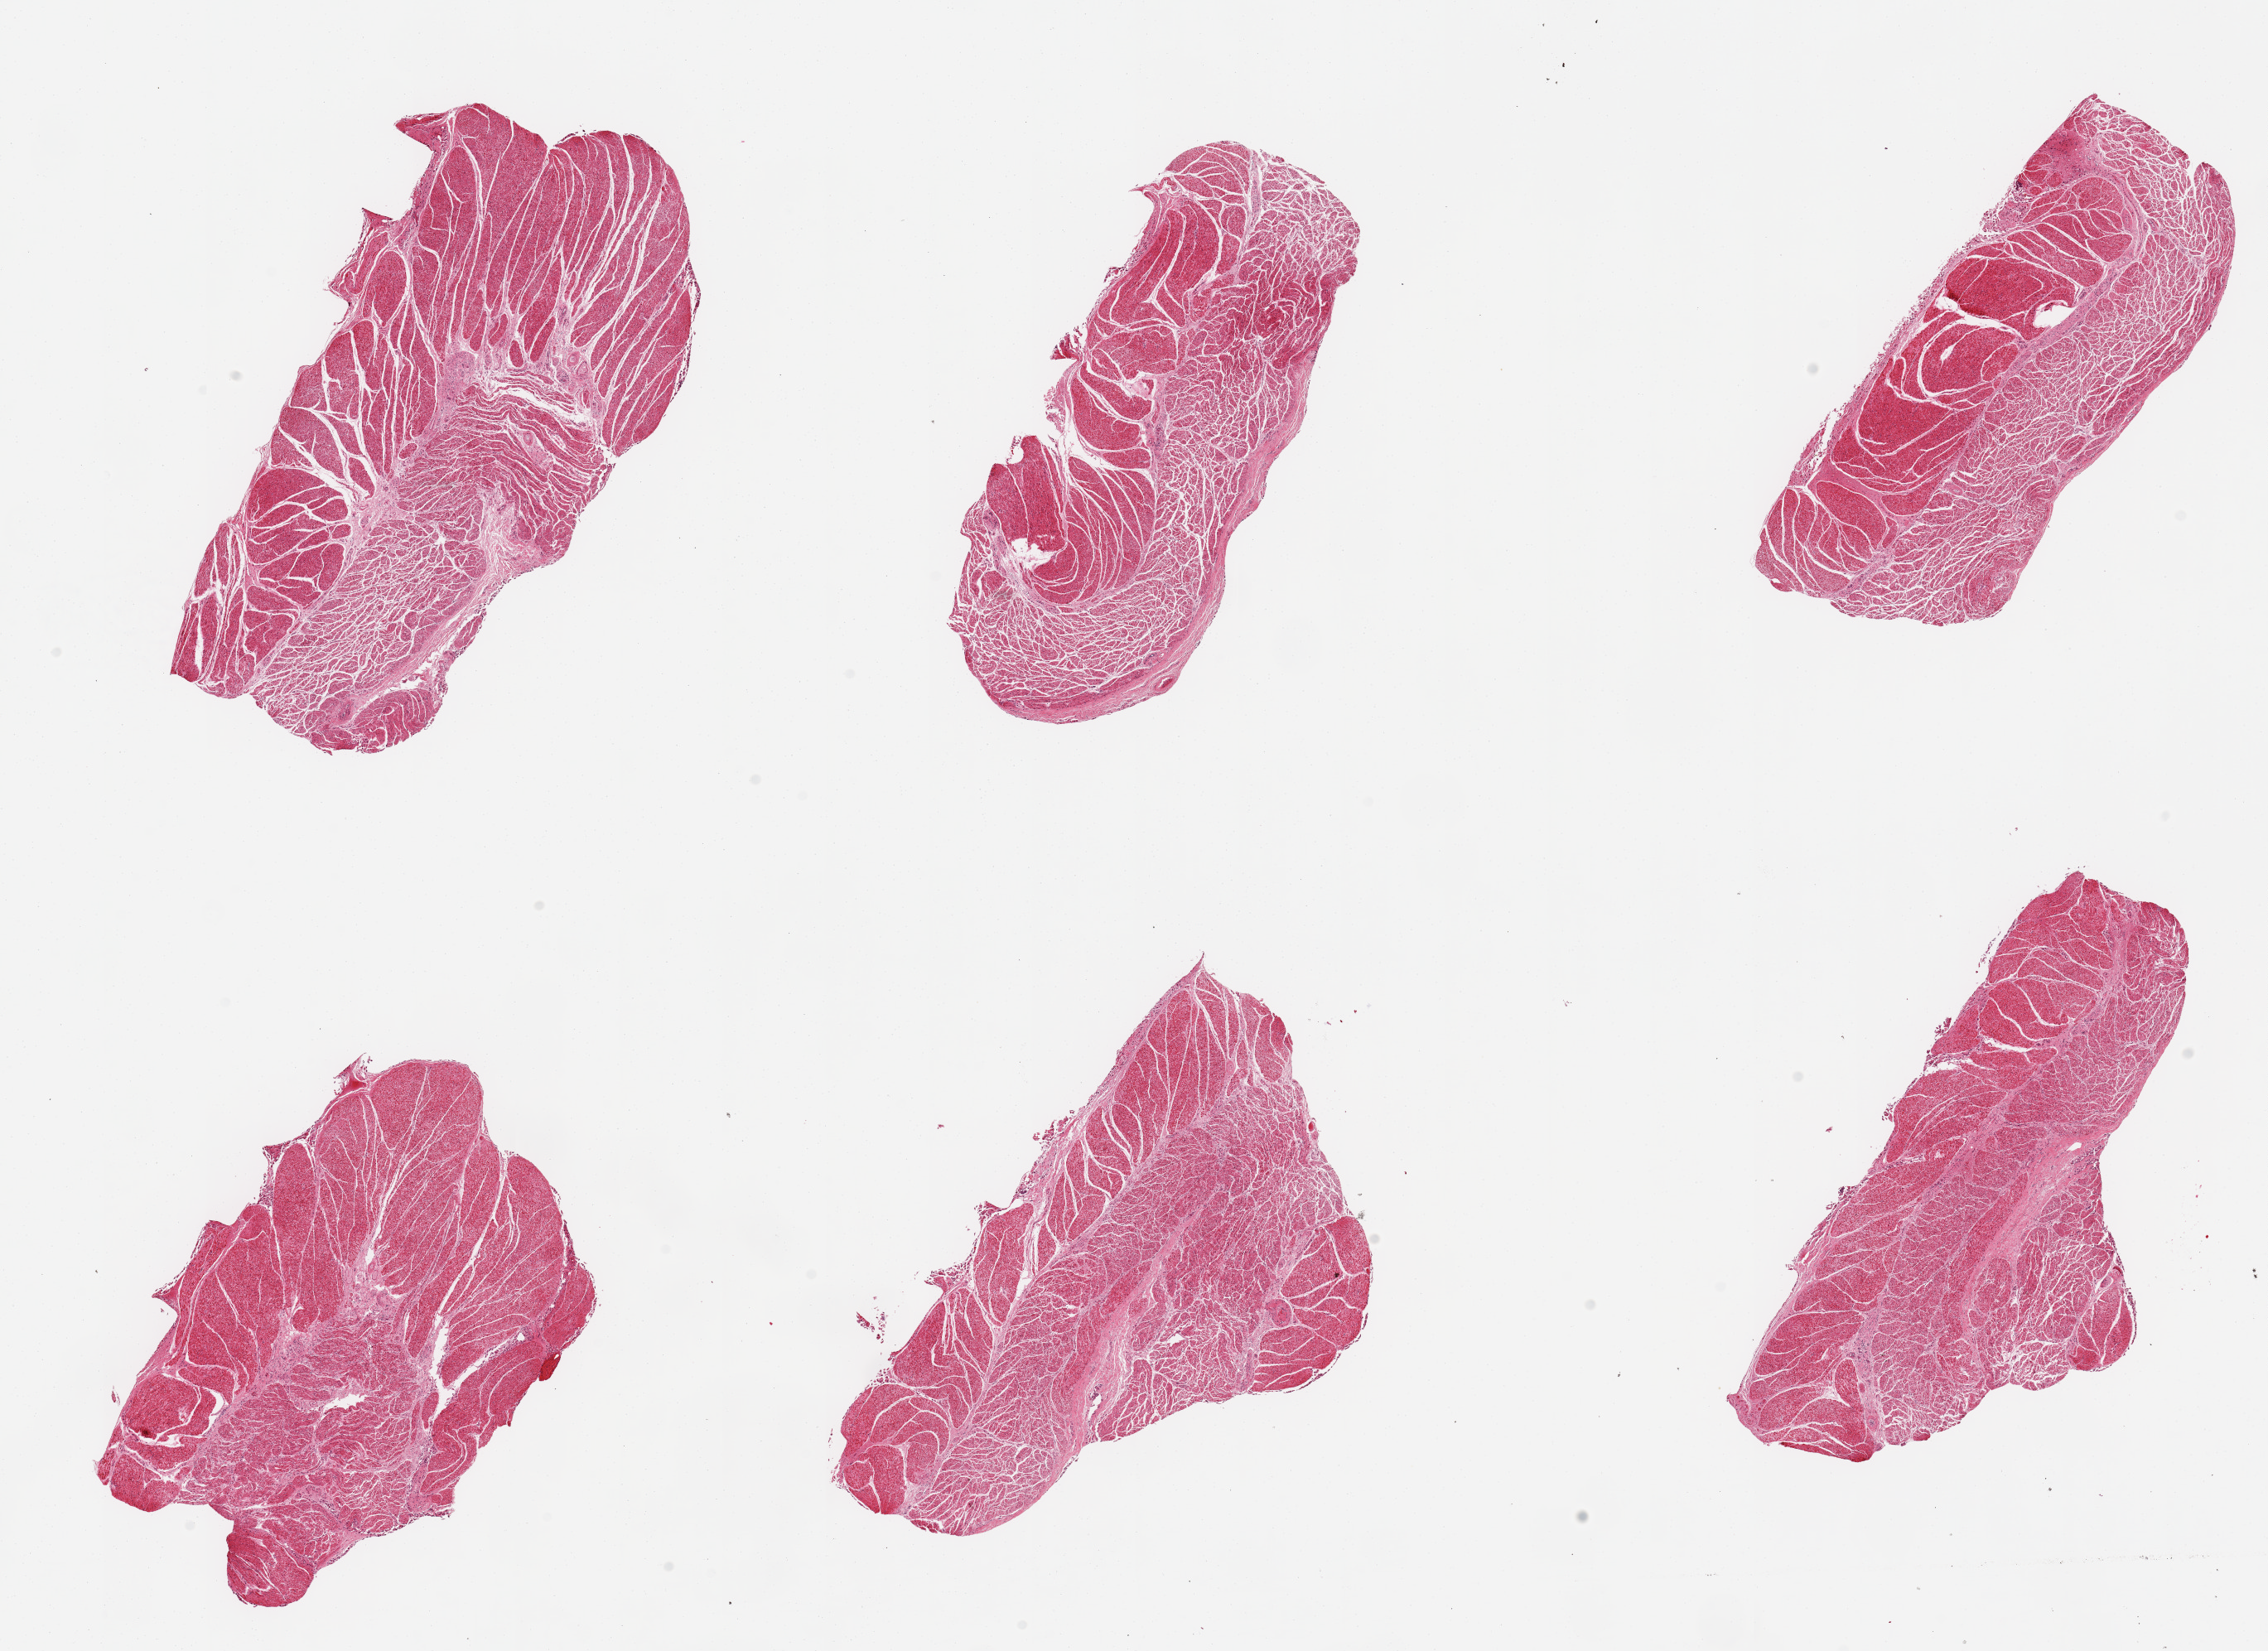
Hematoxylin and eosin (H&E) whole-slide image, brightfield — low-resolution overview of the scanned area, about 21.7 x 15.8 mm (acquisition: 20x scan). PAXgene-fixed, paraffin-embedded tissue. Target tissue: gastroesophageal junction. Tissue donor sample. Donor: female.
Review note (as recorded): 6 pieces, confirmed target muscularis.